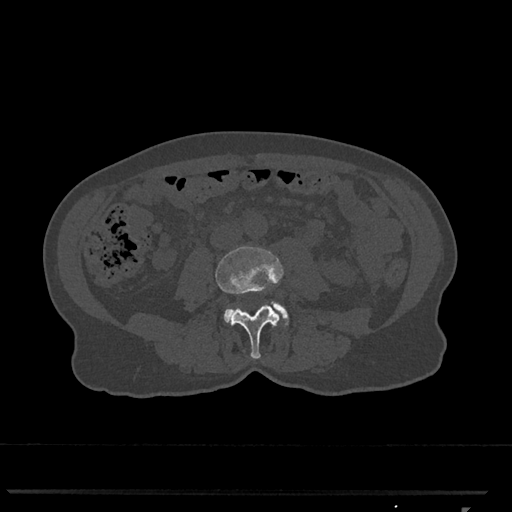
CT including the spine, one axial slice. Slice 253 of 793 in the series (ordered by position). 120 kVp. Bone window (W 1800 / L 400 HU). 512 × 512 image matrix. Patient: female, 62 years. From the clinical record (not read from this slice): primary cancer: renal.
Structures marked on this image (semi-automatically segmented with operator editing):
- L3 vertebra: bounding box (x1, y1, x2, y2) in pixels: (215, 246, 284, 359)
- L4 vertebra: (224, 302, 289, 325)